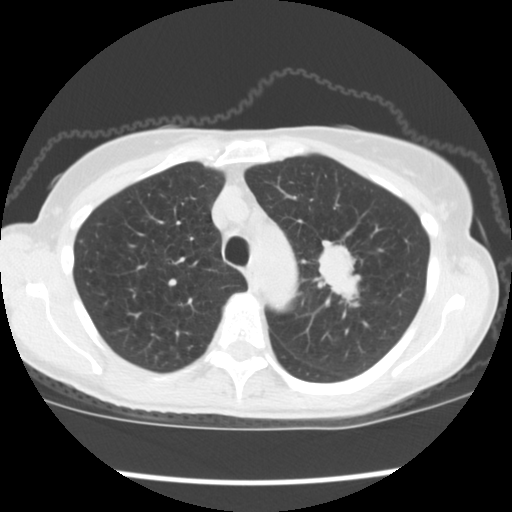
Low-dose screening chest CT, one axial slice; position 139 of 176 along the scan axis; reconstruction kernel STANDARD; 120 kVp; lung window (W 1500 / L -600 HU); 2.5 mm slice thickness; 512 × 512 image matrix, field of view 318 × 318 mm.
Structures marked on this image (outlined manually by an expert reader):
- lesion 1 (tumor, upper lobe of left lung): bounding box (x1, y1, x2, y2) in pixels: (318, 240, 361, 302)